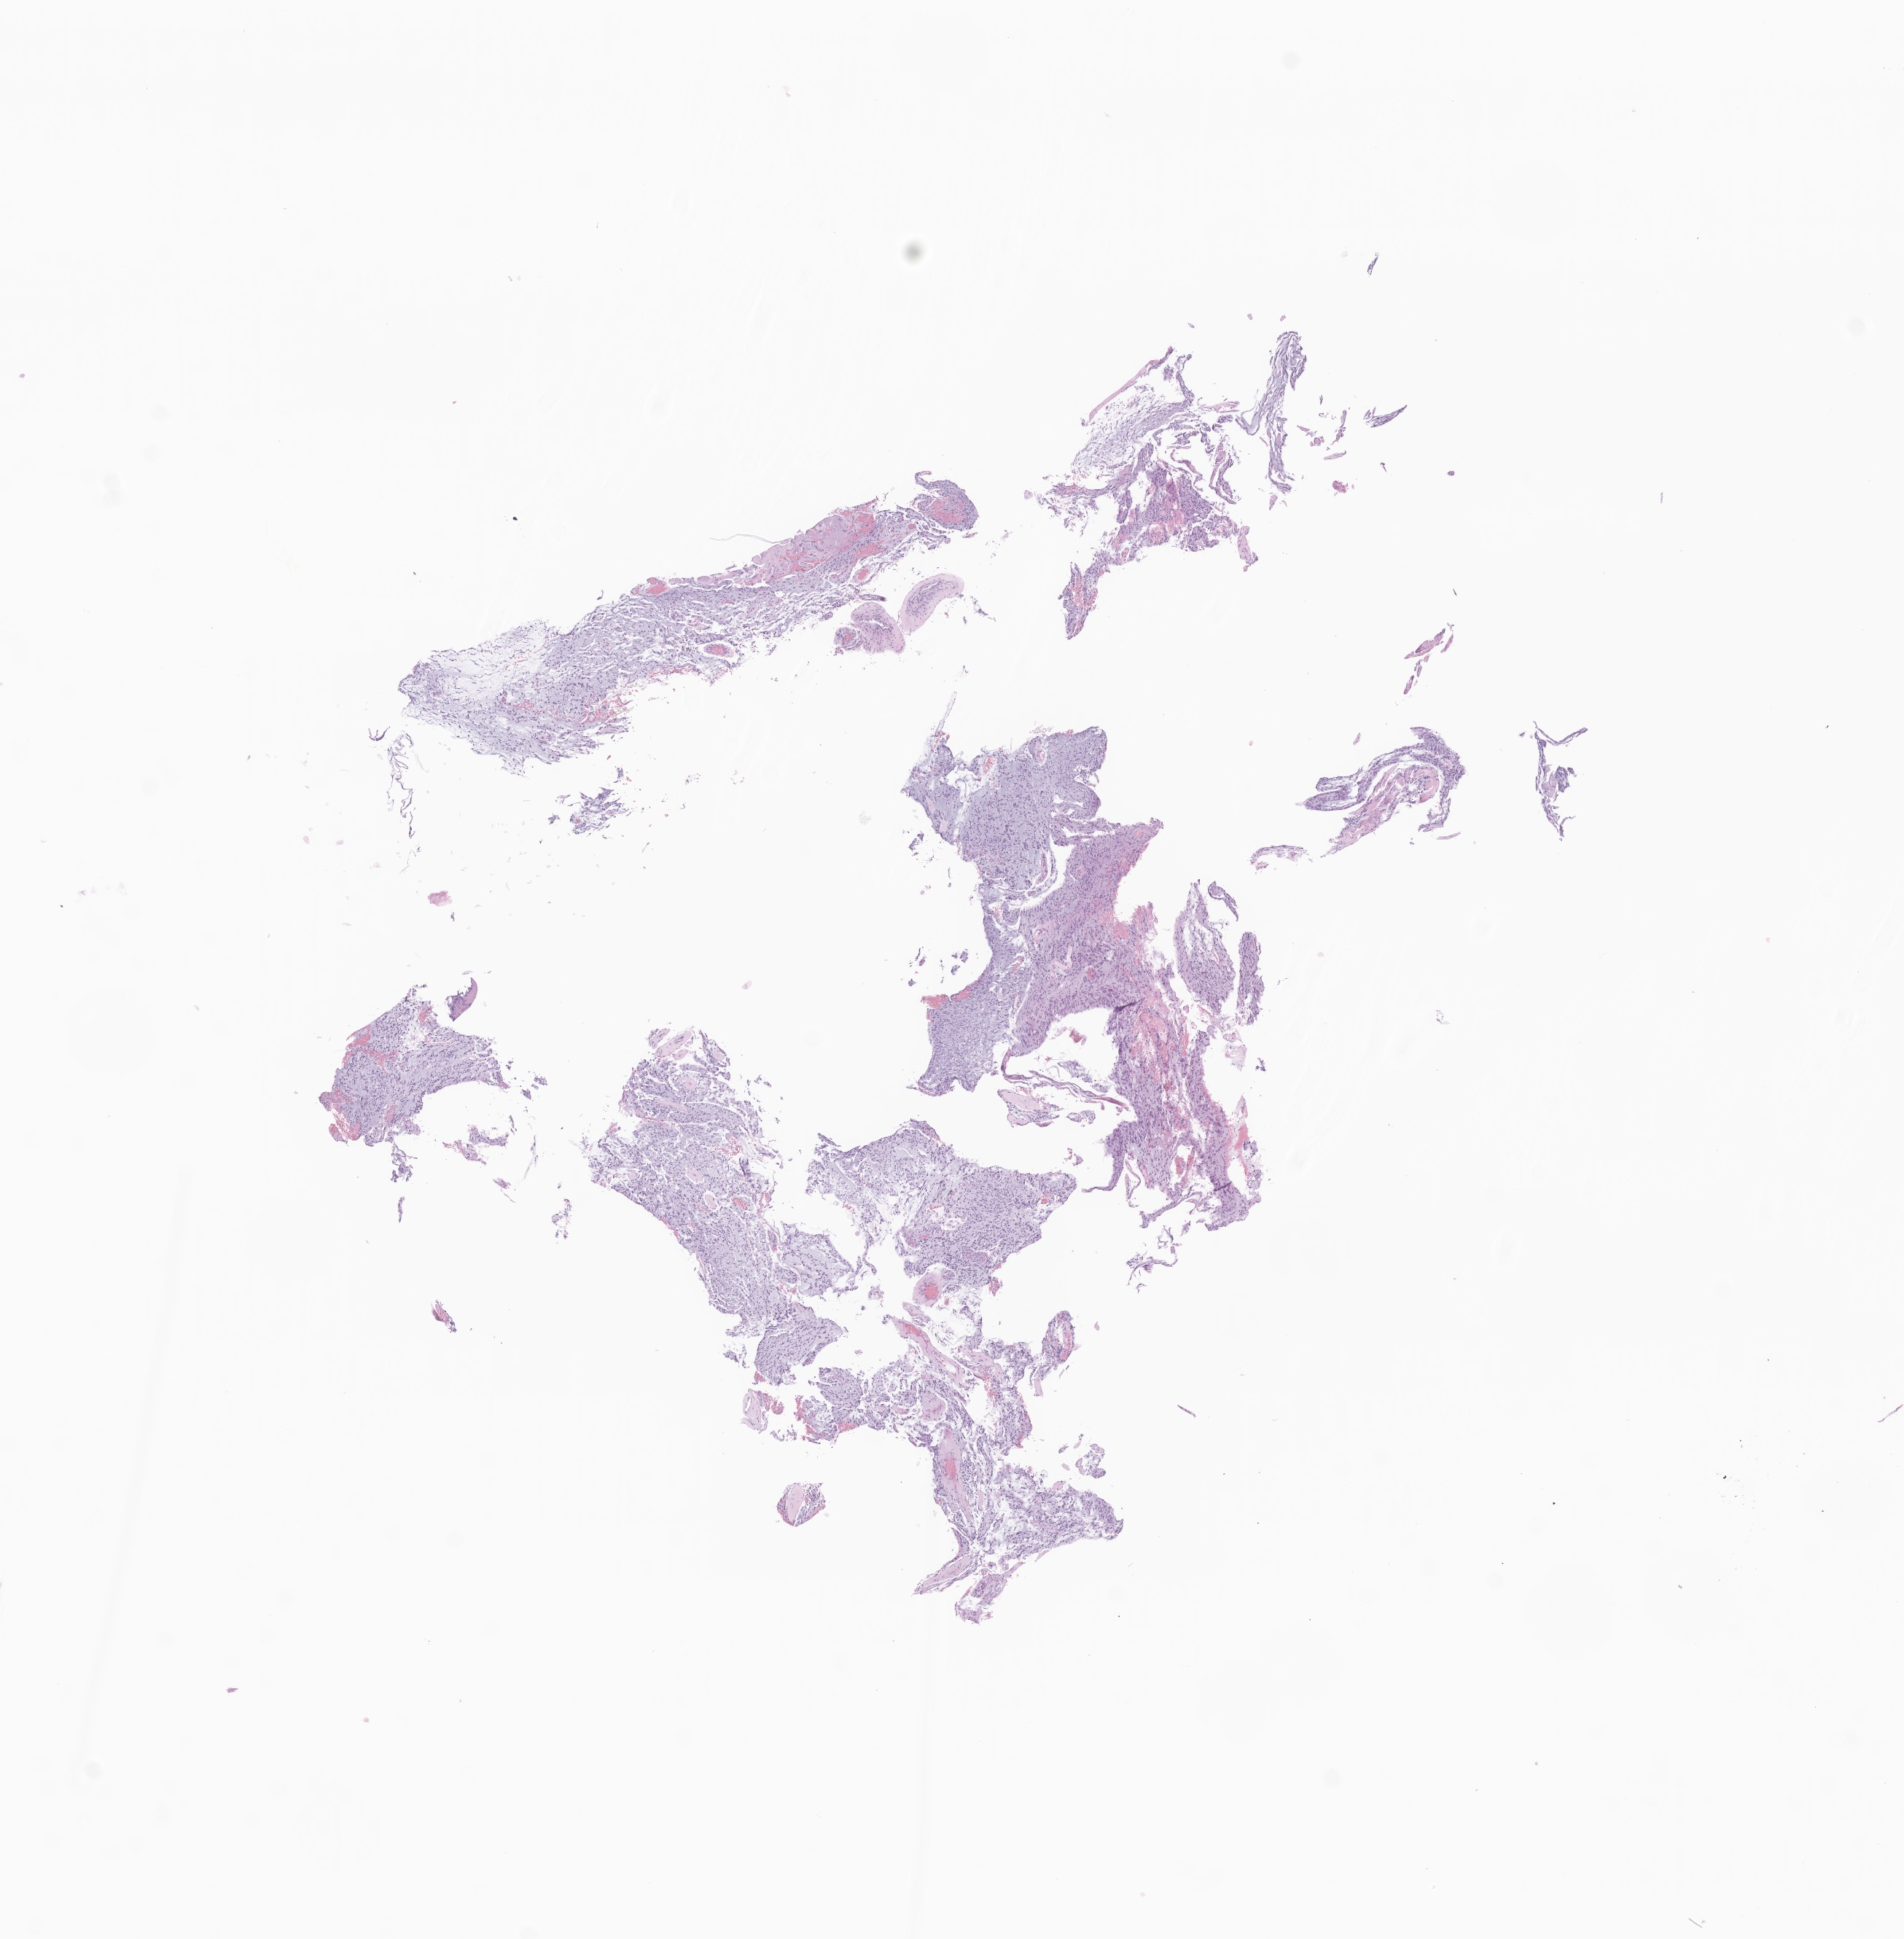
Hematoxylin and eosin (H&E) whole-slide image of tumor tissue from the spinal cord — shown as a low-resolution overview of the whole scanned area (about 11.0 x 11.2 mm). Formalin-fixed, paraffin-embedded (FFPE) tissue. Patient: male, age 98 months (8 years 2 months).
Recorded diagnosis: Glioma, malignant.